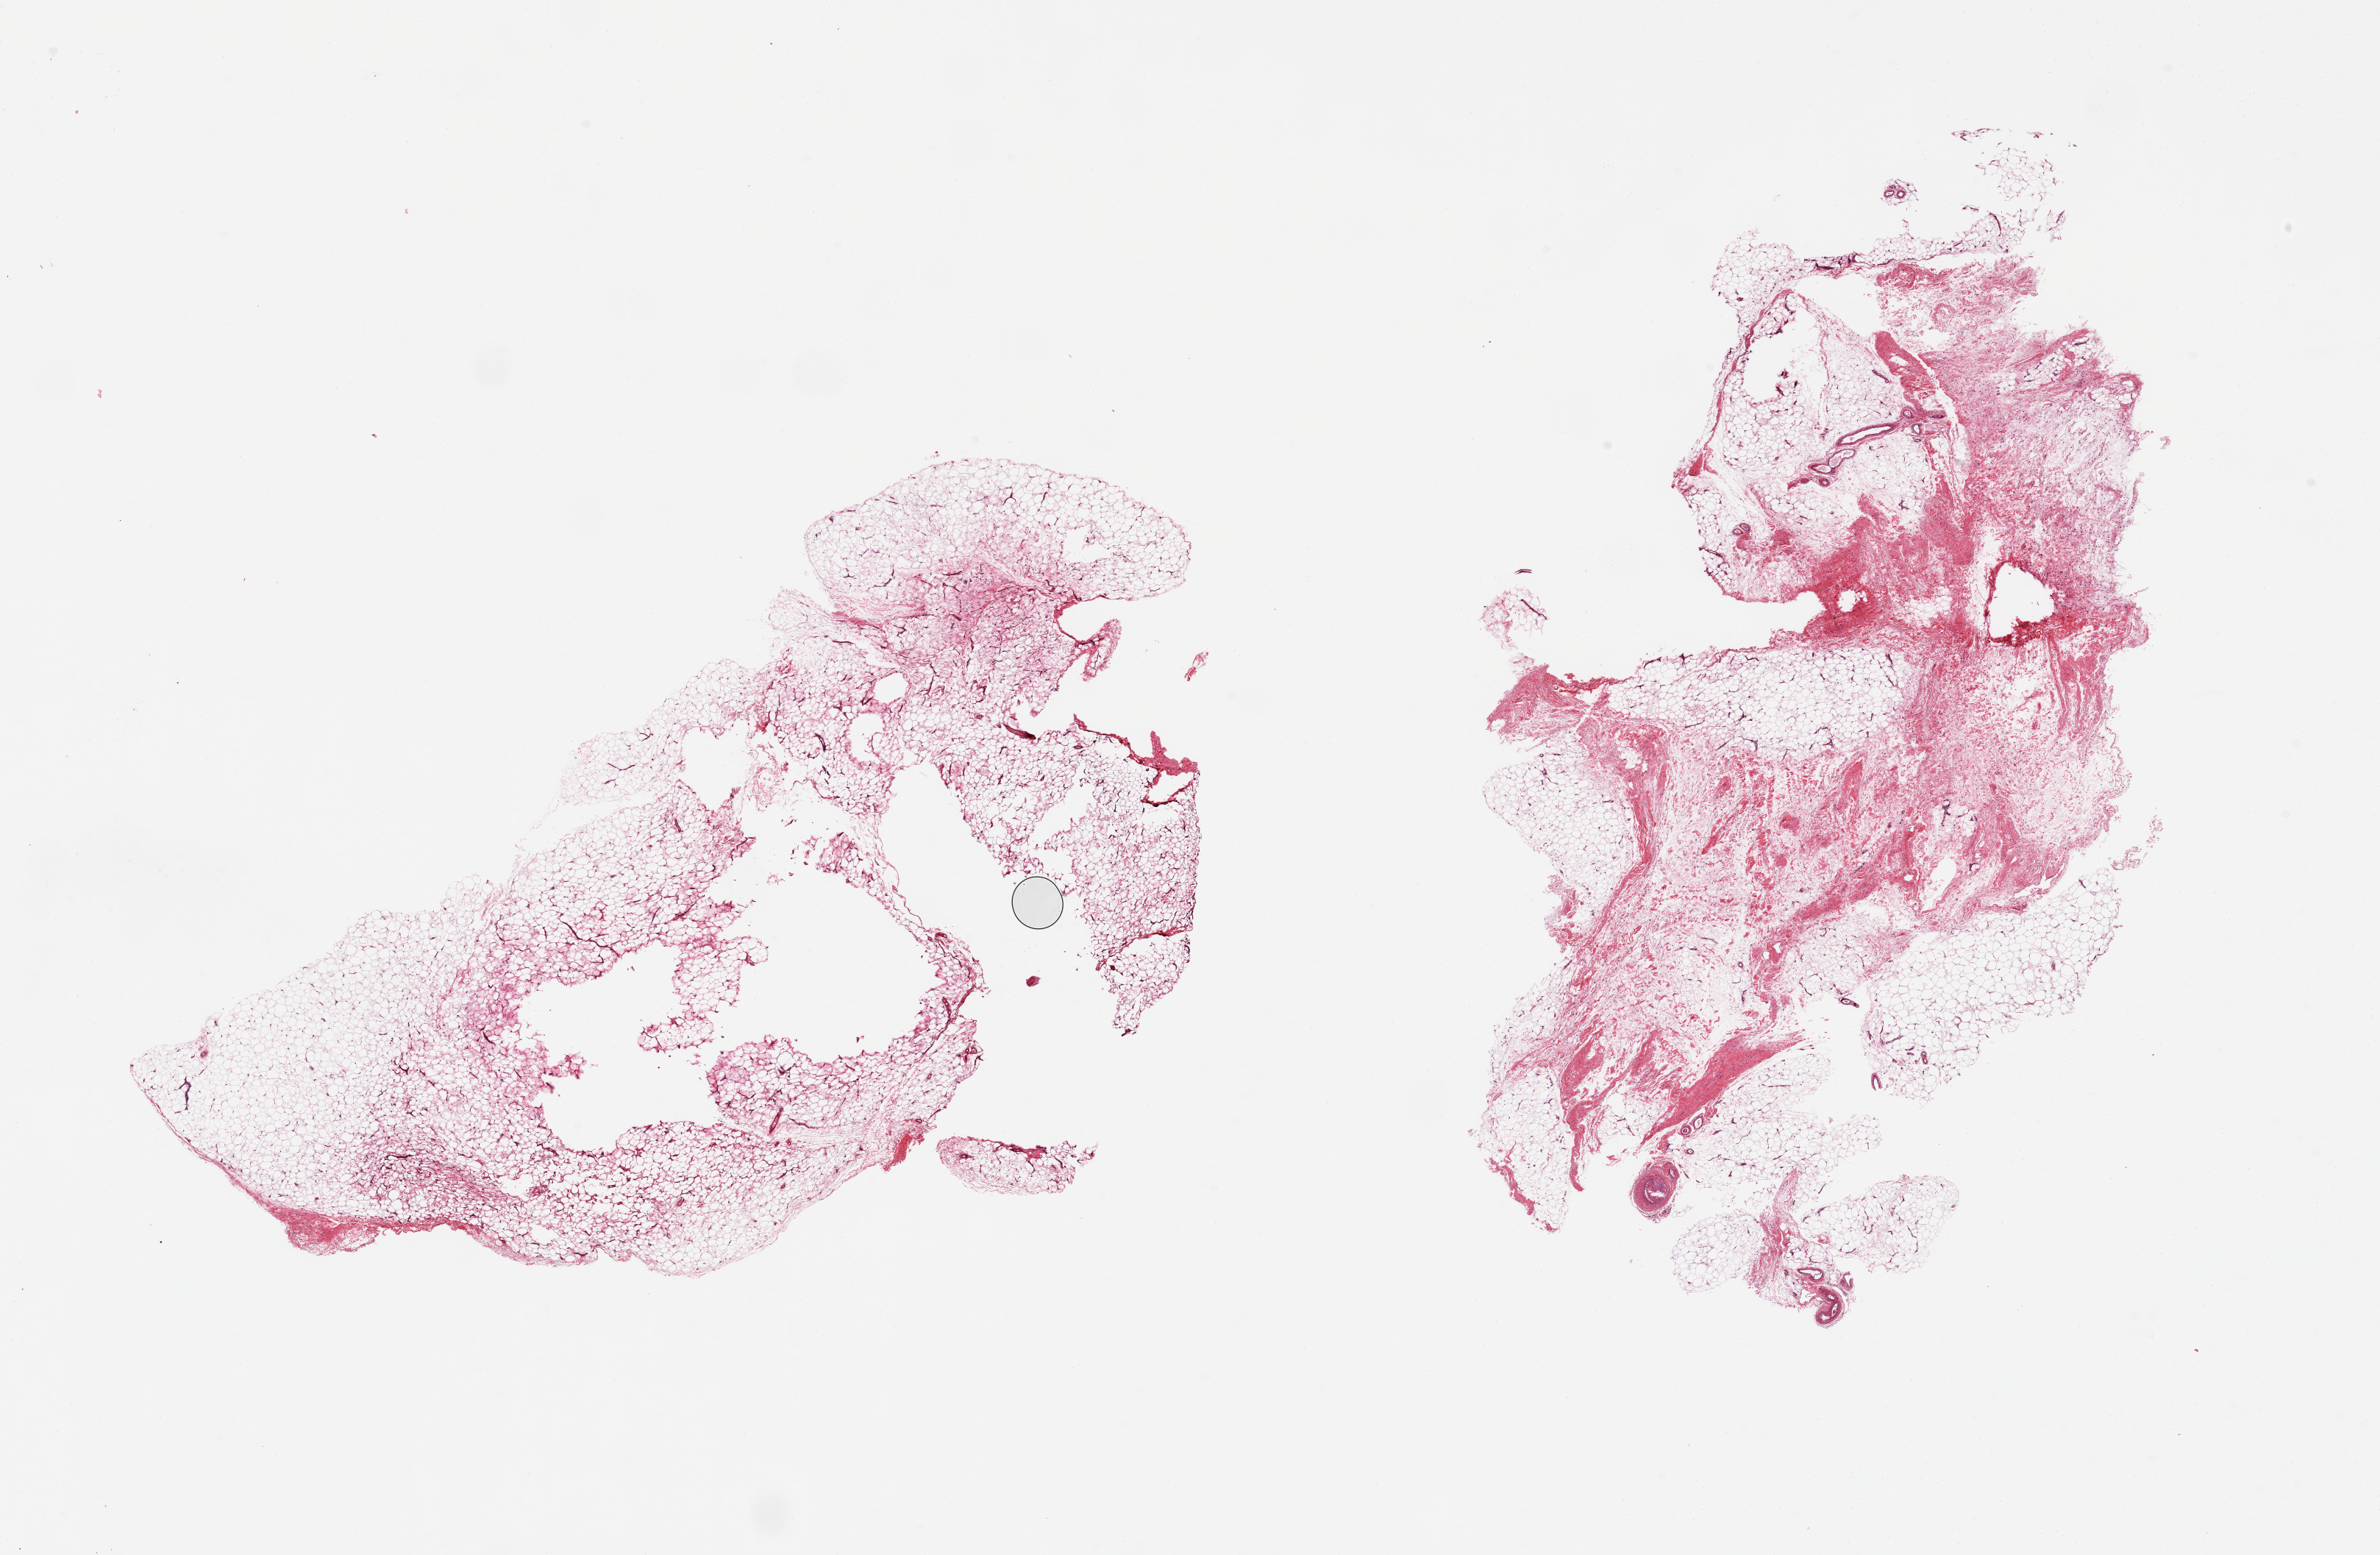
Digitized H&E-stained section — shown as a low-resolution overview of the whole scanned area (about 25.6 x 16.7 mm), PAXgene-fixed paraffin-embedded (PFPE) section, sampled site (target tissue): adipose tissue, donor tissue sample. Male donor.
Reviewer comment on this tissue sample: 2 pieces; 10% and 25% fibrovascular component; one sample with numerous empty spaces.